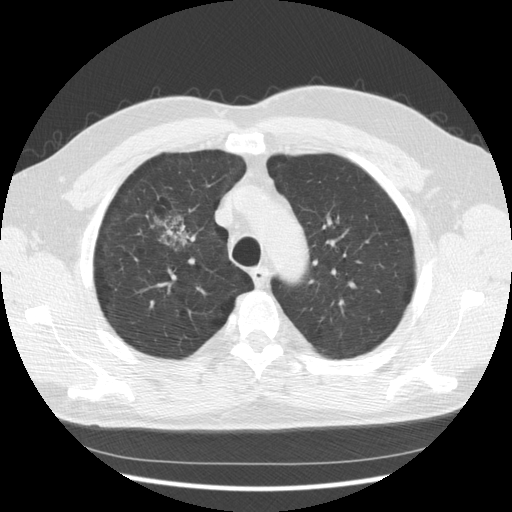
Axial slice from a low-dose chest CT screening exam. Third annual screen. Lung window (W 1500 / L -600 HU). Standard (soft-tissue) reconstruction kernel (STANDARD). 140 kVp. Slice 96 of 133 in the series. 512 × 512 image matrix, field of view 369 × 369 mm. Male participant, aged 60 years at enrolment. Former smoker at enrolment.
Expert-annotated lung lesion, bounding box [x1, y1, x2, y2] px = [141, 201, 201, 267]. The exam's reader record, not a measurement of the box and not confirmed to be the same lesion: non-calcified nodule or mass ≥4 mm, right upper lobe, poorly defined margins, mixed attenuation, pre-existing on the prior screen: yes; interval growth: yes. Lung cancer was diagnosed 121 days after this screen: papillary adenocarcinoma, NOS, right upper lobe, moderately differentiated (G2), stage IB (AJCC 6th edition), 32 mm at pathology.